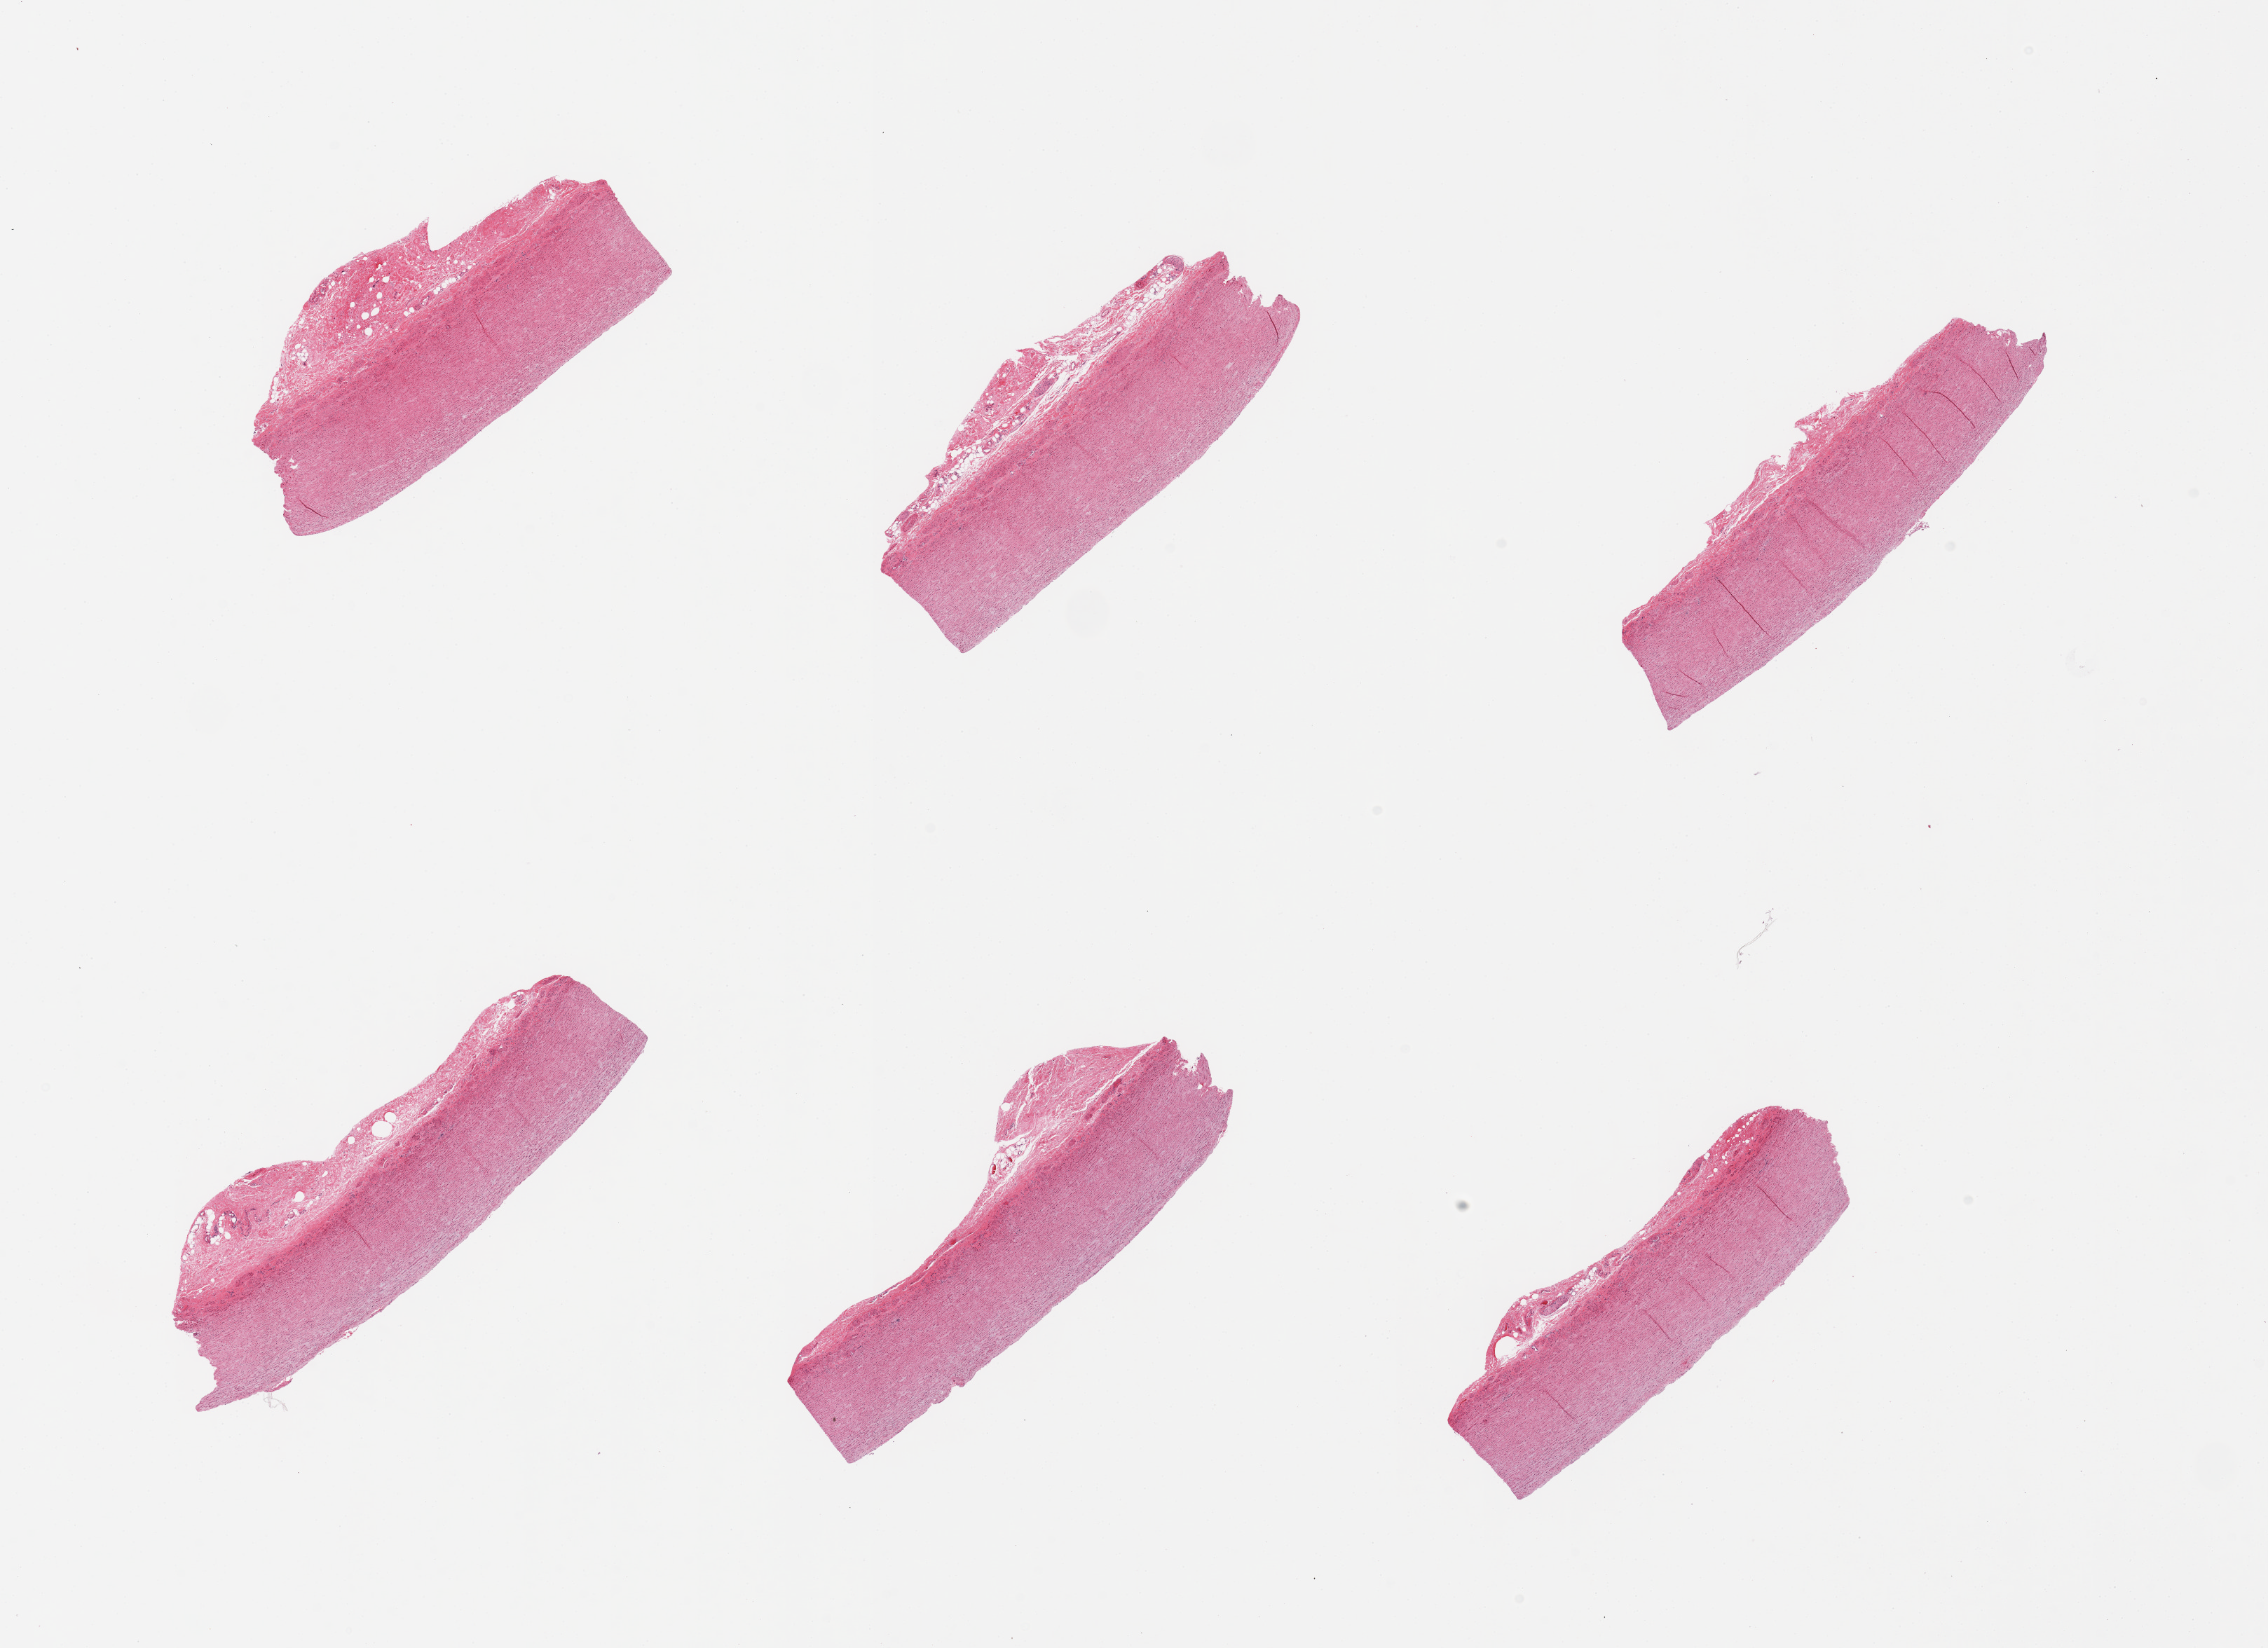
Haematoxylin and eosin whole-slide image, low-resolution overview of the scanned area, about 25.6 x 18.6 mm, PAXgene-fixed paraffin-embedded (PFPE) section, target tissue: aorta, donor tissue sample. Donor sex: male.
• pathologist's review note for this sample: 6 pieces, adherent serosa/fat up to ~1mm